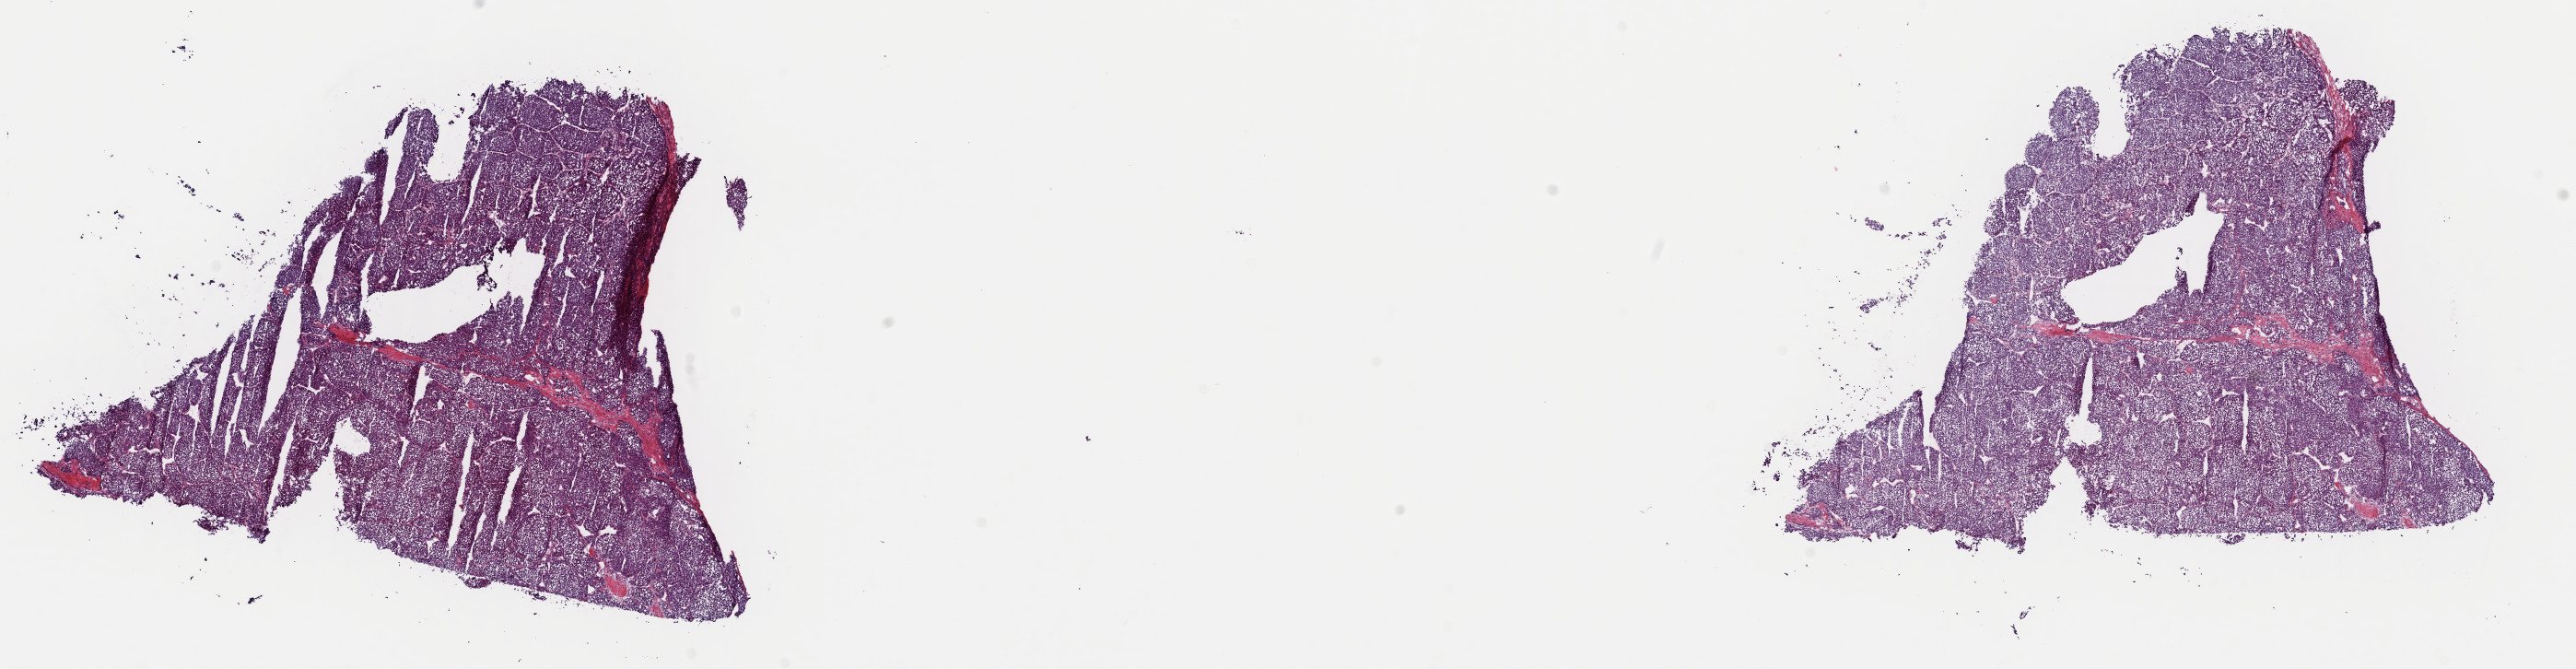
Digitized H&E-stained tissue section (whole slide) — low-resolution overview of the scanned area, about 22.1 x 5.7 mm (slide scanned at 40x), frozen section from the top of the tissue portion, primary tumour sample from the liver. Patient: female, age at initial diagnosis 51 years. Histologic grade: G3 (poorly differentiated). Slide review estimates, as recorded: tumour cells 90%, tumour nuclei 95%, normal cells 0%, stromal cells 9%, necrosis 1%. Infiltration values recorded for this section: lymphocyte infiltration 1%, monocyte infiltration 2%, neutrophil infiltration 0%.
AJCC pathologic stage: IIIA. Histologic diagnosis: Hepatocellular carcinoma, NOS.